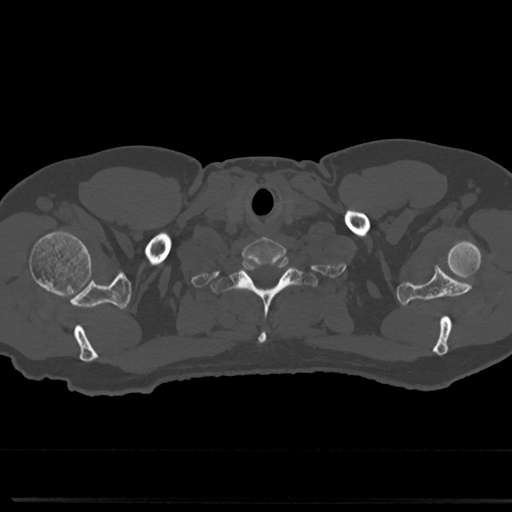
CT including the spine, one axial slice. Position 683 of 817 along the scan axis. 120 kVp. Bone window (W 1800 / L 400 HU). 0.5 mm slice thickness. 512 × 512 image matrix. Male patient, age 61 years. Case-level facts recorded for this patient, not image findings: primary cancer: prostate.
Annotated regions visible in this slice (semi-automatically segmented with operator editing):
- T1 vertebra: bounding box <219,255,312,345> (left, top, right, bottom; pixels)